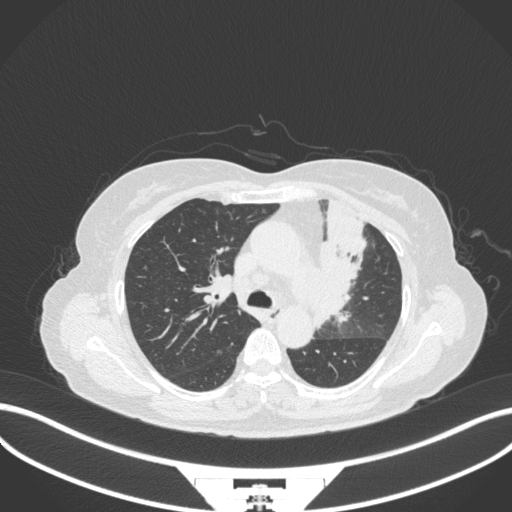
Chest CT, one axial slice. Slice 224 of 382 in the series (ordered by position). Reconstruction kernel B31f. 120 kVp. Lung window (W 1500 / L -600 HU). 1 mm slice thickness. 512 × 512 image matrix, field of view 400 × 400 mm. Patient: female, 64 years. Case-level facts recorded for this patient, not image findings: clinical TNM (as recorded): T2a N2 M0.
Outlined on this slice (rectangle marked by the reading radiologist):
- lung tumour (recorded histology: adenocarcinoma): box from (x=310, y=199) to (x=369, y=332) px